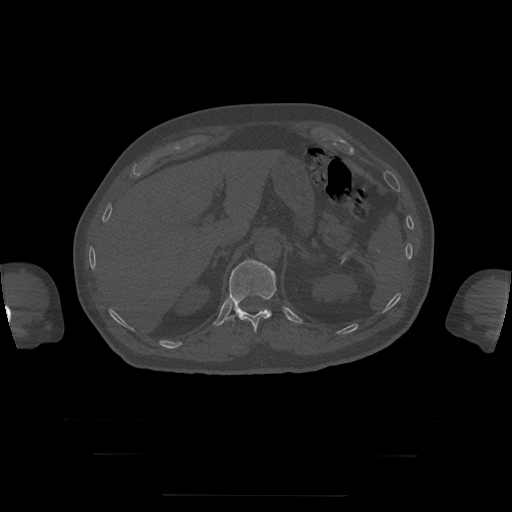
CT including the spine, one axial slice. Reconstruction kernel STANDARD. 120 kVp. Bone window (W 1800 / L 400 HU). 512 × 512 image matrix. Patient age 73 years. Case-level facts recorded for this patient, not image findings: primary cancer: prostate.
Structures marked on this image (semi-automatic segmentation, software-assisted and operator-edited):
- T12 vertebra: bounding box [x1, y1, x2, y2] px = [228, 260, 276, 333]